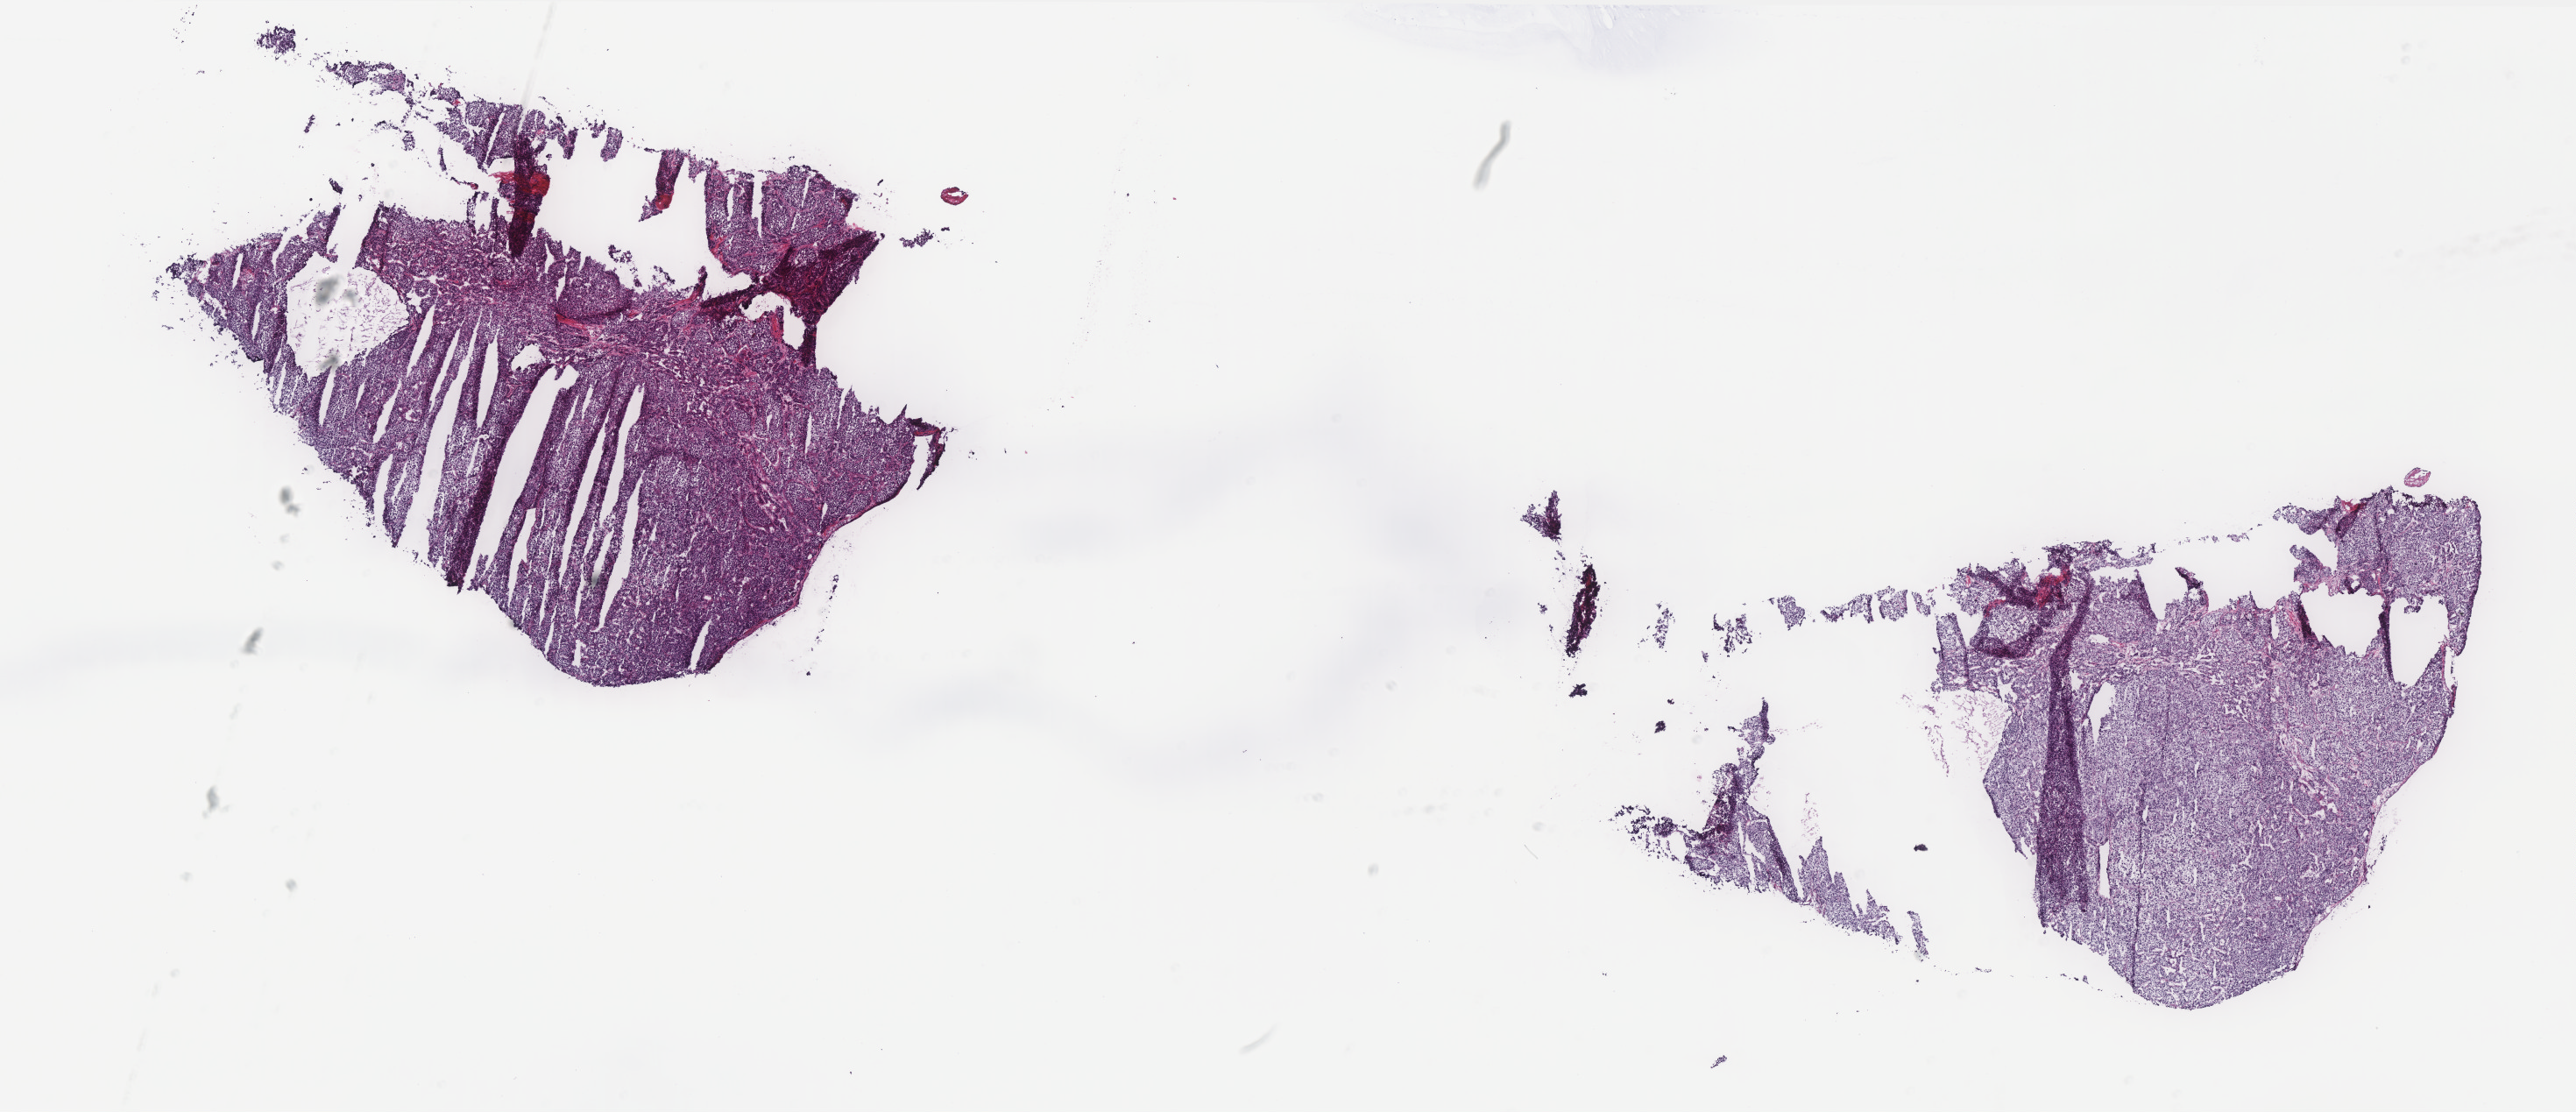
Digitized Hematoxylin and eosin (H&E) stained tissue section (whole slide) — a low-resolution overview of the entire scanned area, about 23.6 x 10.2 mm; frozen section from the top of the tissue portion; primary tumour sample from the liver. Patient: male, age at initial diagnosis 23 years. Histologic grade: G3 (poorly differentiated). Pathologist review of this section (percent, as recorded): tumour cells 85%, tumour nuclei 85%, normal cells 0%, stromal cells 15%, necrosis 0%. Infiltration values recorded for this section: lymphocyte infiltration 5%, monocyte infiltration 0%, neutrophil infiltration 0%.
• histologic diagnosis: Hepatocellular carcinoma, NOS
• AJCC pathologic stage: III (6th edition)